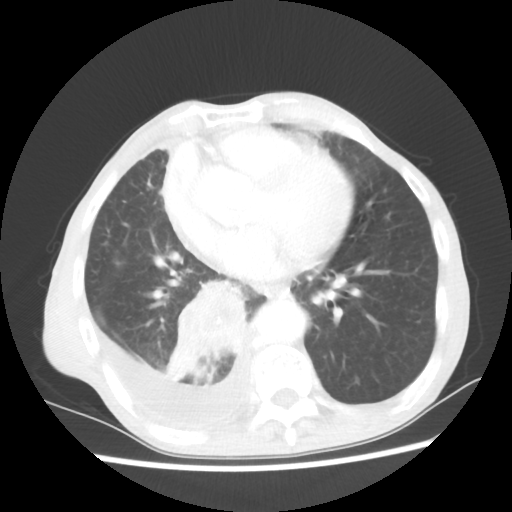
Chest CT, one axial slice; lung window (W 1500 / L -600 HU); 5 mm slice thickness; 512 × 512 image matrix, field of view 335 × 335 mm. Patient: male, 76 years. From the clinical record (not read from this slice): clinical TNM (as recorded): T3 N3 M1a.
Structures marked on this image (bounding box drawn by a radiologist):
- lung tumour (recorded histology: squamous cell carcinoma): bounding box <156,270,251,384> (left, top, right, bottom; pixels)